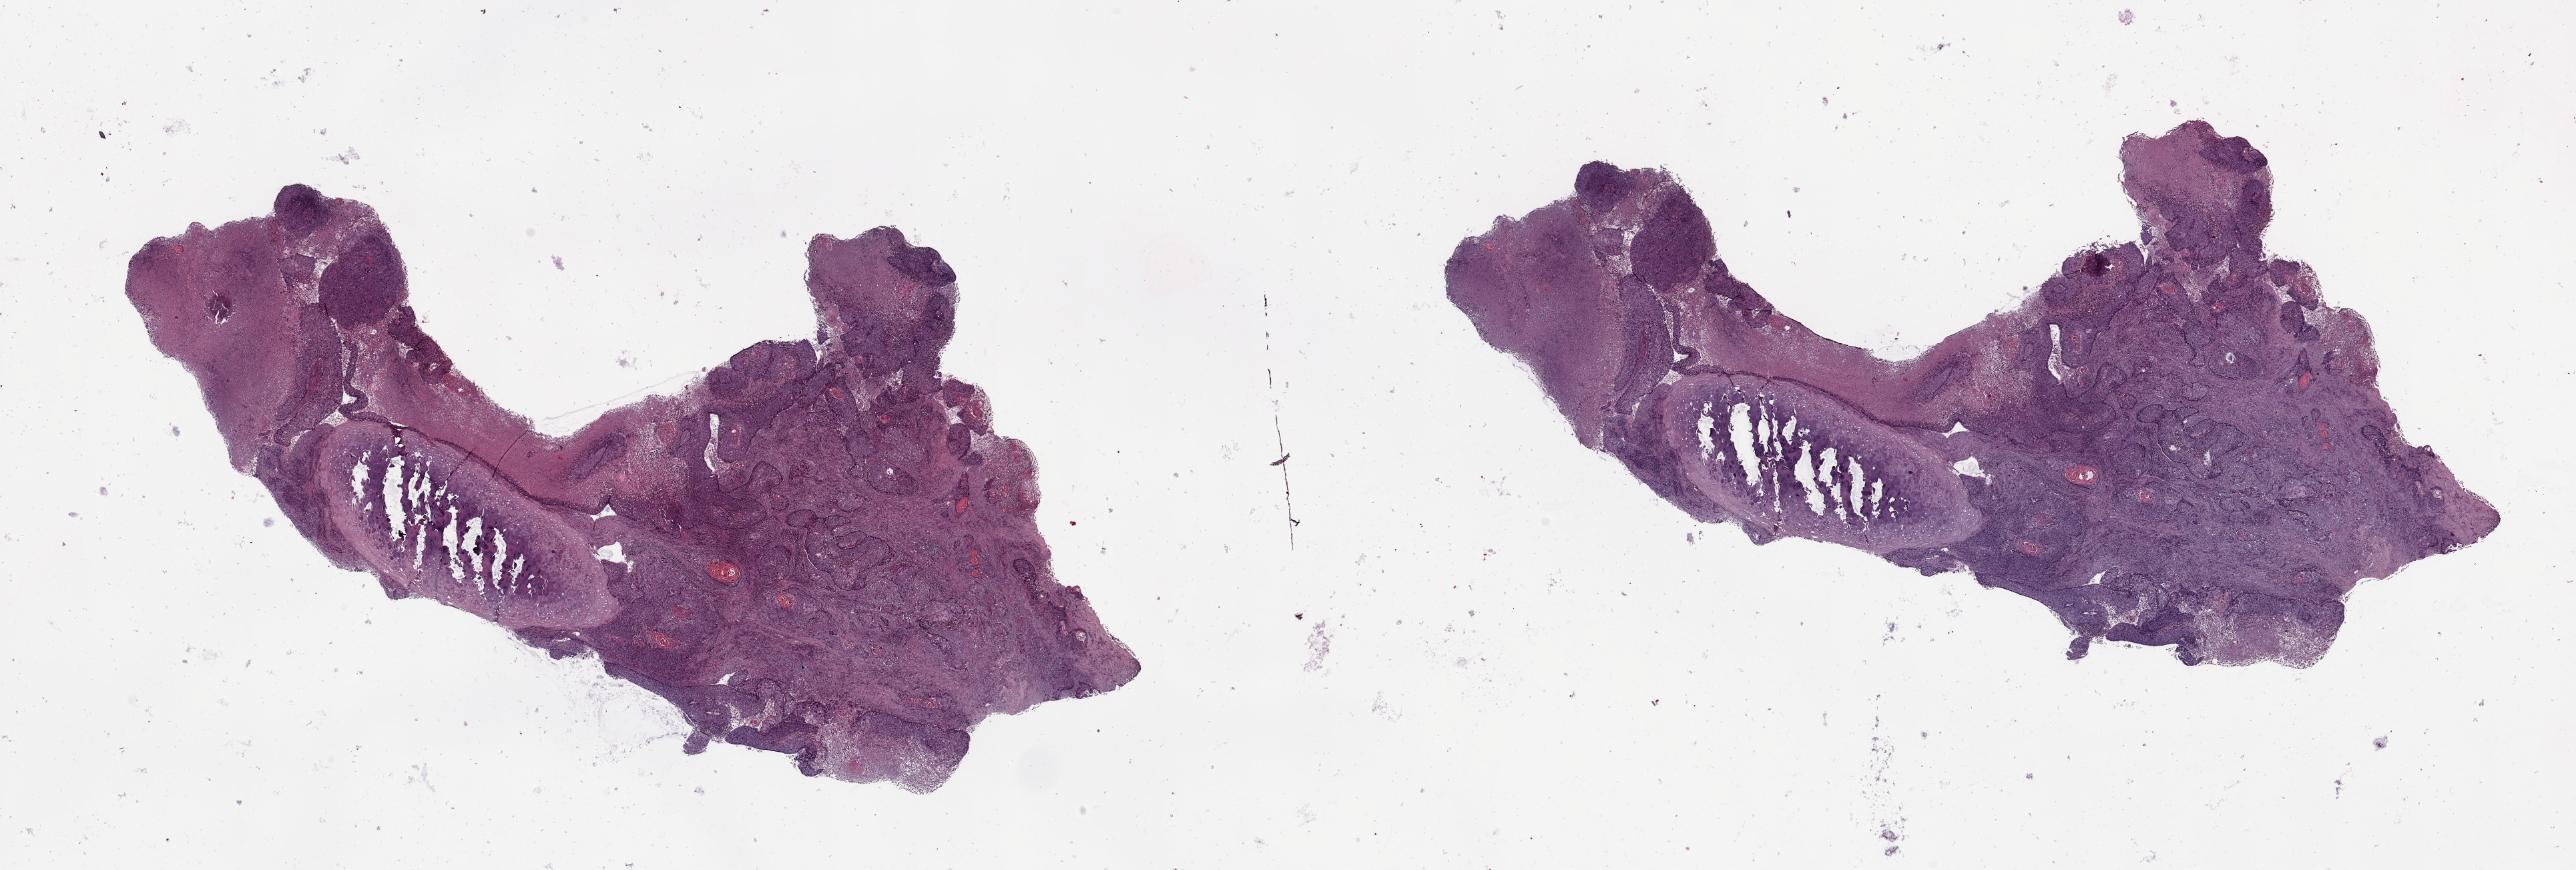
H&E whole-slide image — low-resolution overview of the scanned area, about 30.5 x 10.3 mm (from a 20x scan), tumour tissue sample, lung. Male, 66 y/o. Histologic grade: G2 (moderately differentiated).
Diagnosis: Squamous cell carcinoma, NOS. AJCC pathologic stage: IIA. Primary tumour site (as recorded): left upper lobe.